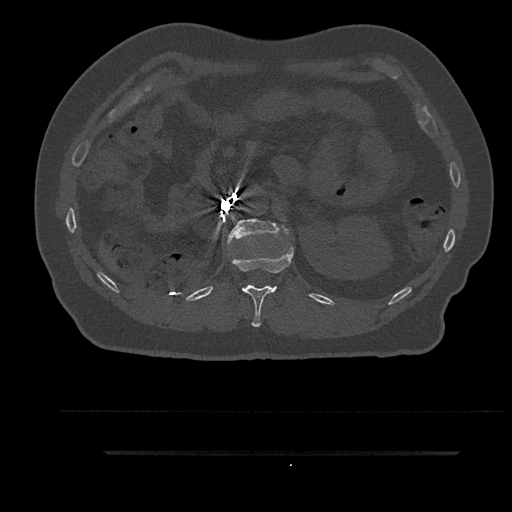
CT including the spine, one axial slice; slice 220 of 797 in the series (ordered by position); 120 kVp; bone window (W 1800 / L 400 HU); 512 × 512 image matrix, field of view 432 × 432 mm. Patient: male, 63 years. From the clinical record (not read from this slice): primary cancer: renal.
Structures marked on this image (semi-automatic segmentation, software-assisted and operator-edited):
- L1 vertebra: bounding box (x1, y1, x2, y2) in pixels: (227, 219, 289, 245)
- T12 vertebra: (229, 246, 294, 327)